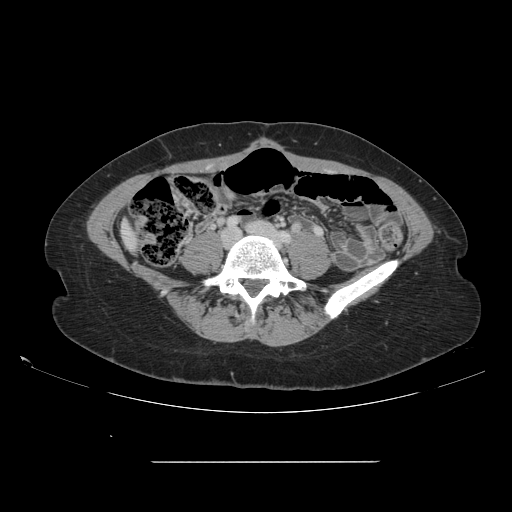
Contrast-enhanced abdominal CT, one axial slice. Position 6 of 151 along the scan axis. Soft-tissue window (W 400 / L 40 HU). 512 × 512 image matrix, field of view 421 × 421 mm. Female patient, age 46 years. From the clinical record (not read from this slice): diagnosis: colorectal cancer liver metastases, imaged before liver resection; multiple liver metastases: yes; largest metastasis: 3 cm.
Structures marked on this image (manually delineated by an expert):
- liver: bounding box (x1, y1, x2, y2) in pixels: (124, 231, 135, 245)
- planned liver remnant (the part of the liver to remain after resection): (125, 228, 134, 244)